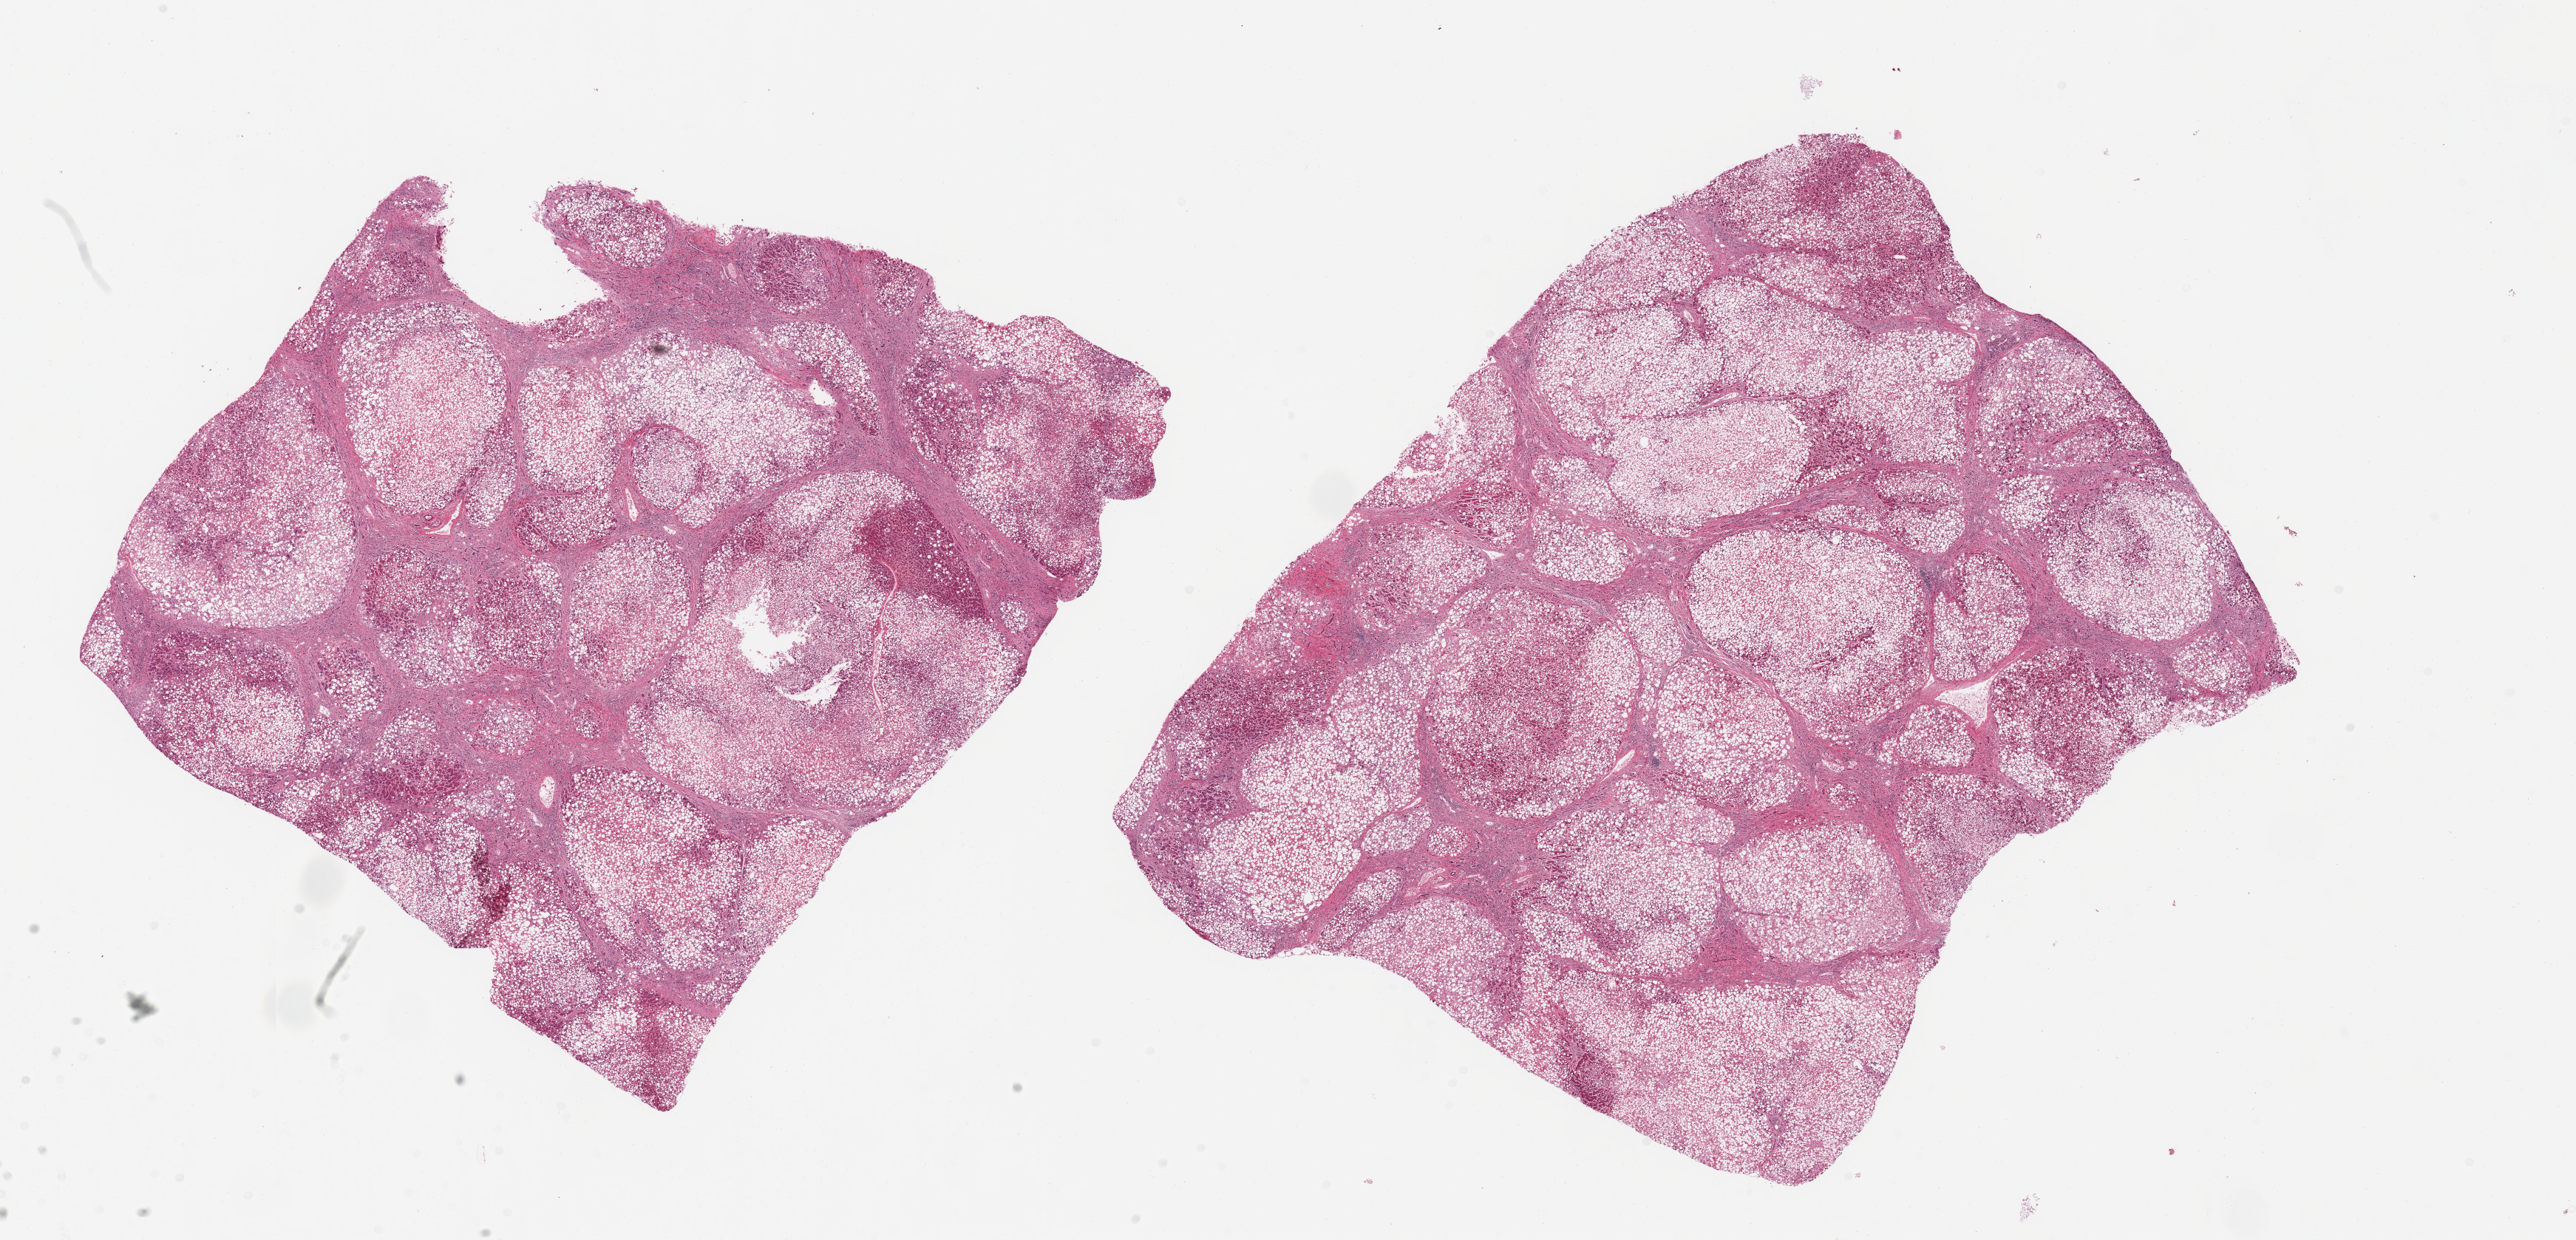
Haematoxylin and eosin whole-slide image, shown as a low-resolution overview of the whole scanned area (about 27.6 x 13.3 mm, slide scanned at 20x); PAXgene-fixed, paraffin-embedded tissue; target tissue: liver; tissue donor sample. Donor sex: male.
• reviewer comment on this tissue sample: 2 pieces, establishc cirrhosis and diffuse macrovesicular steatosis